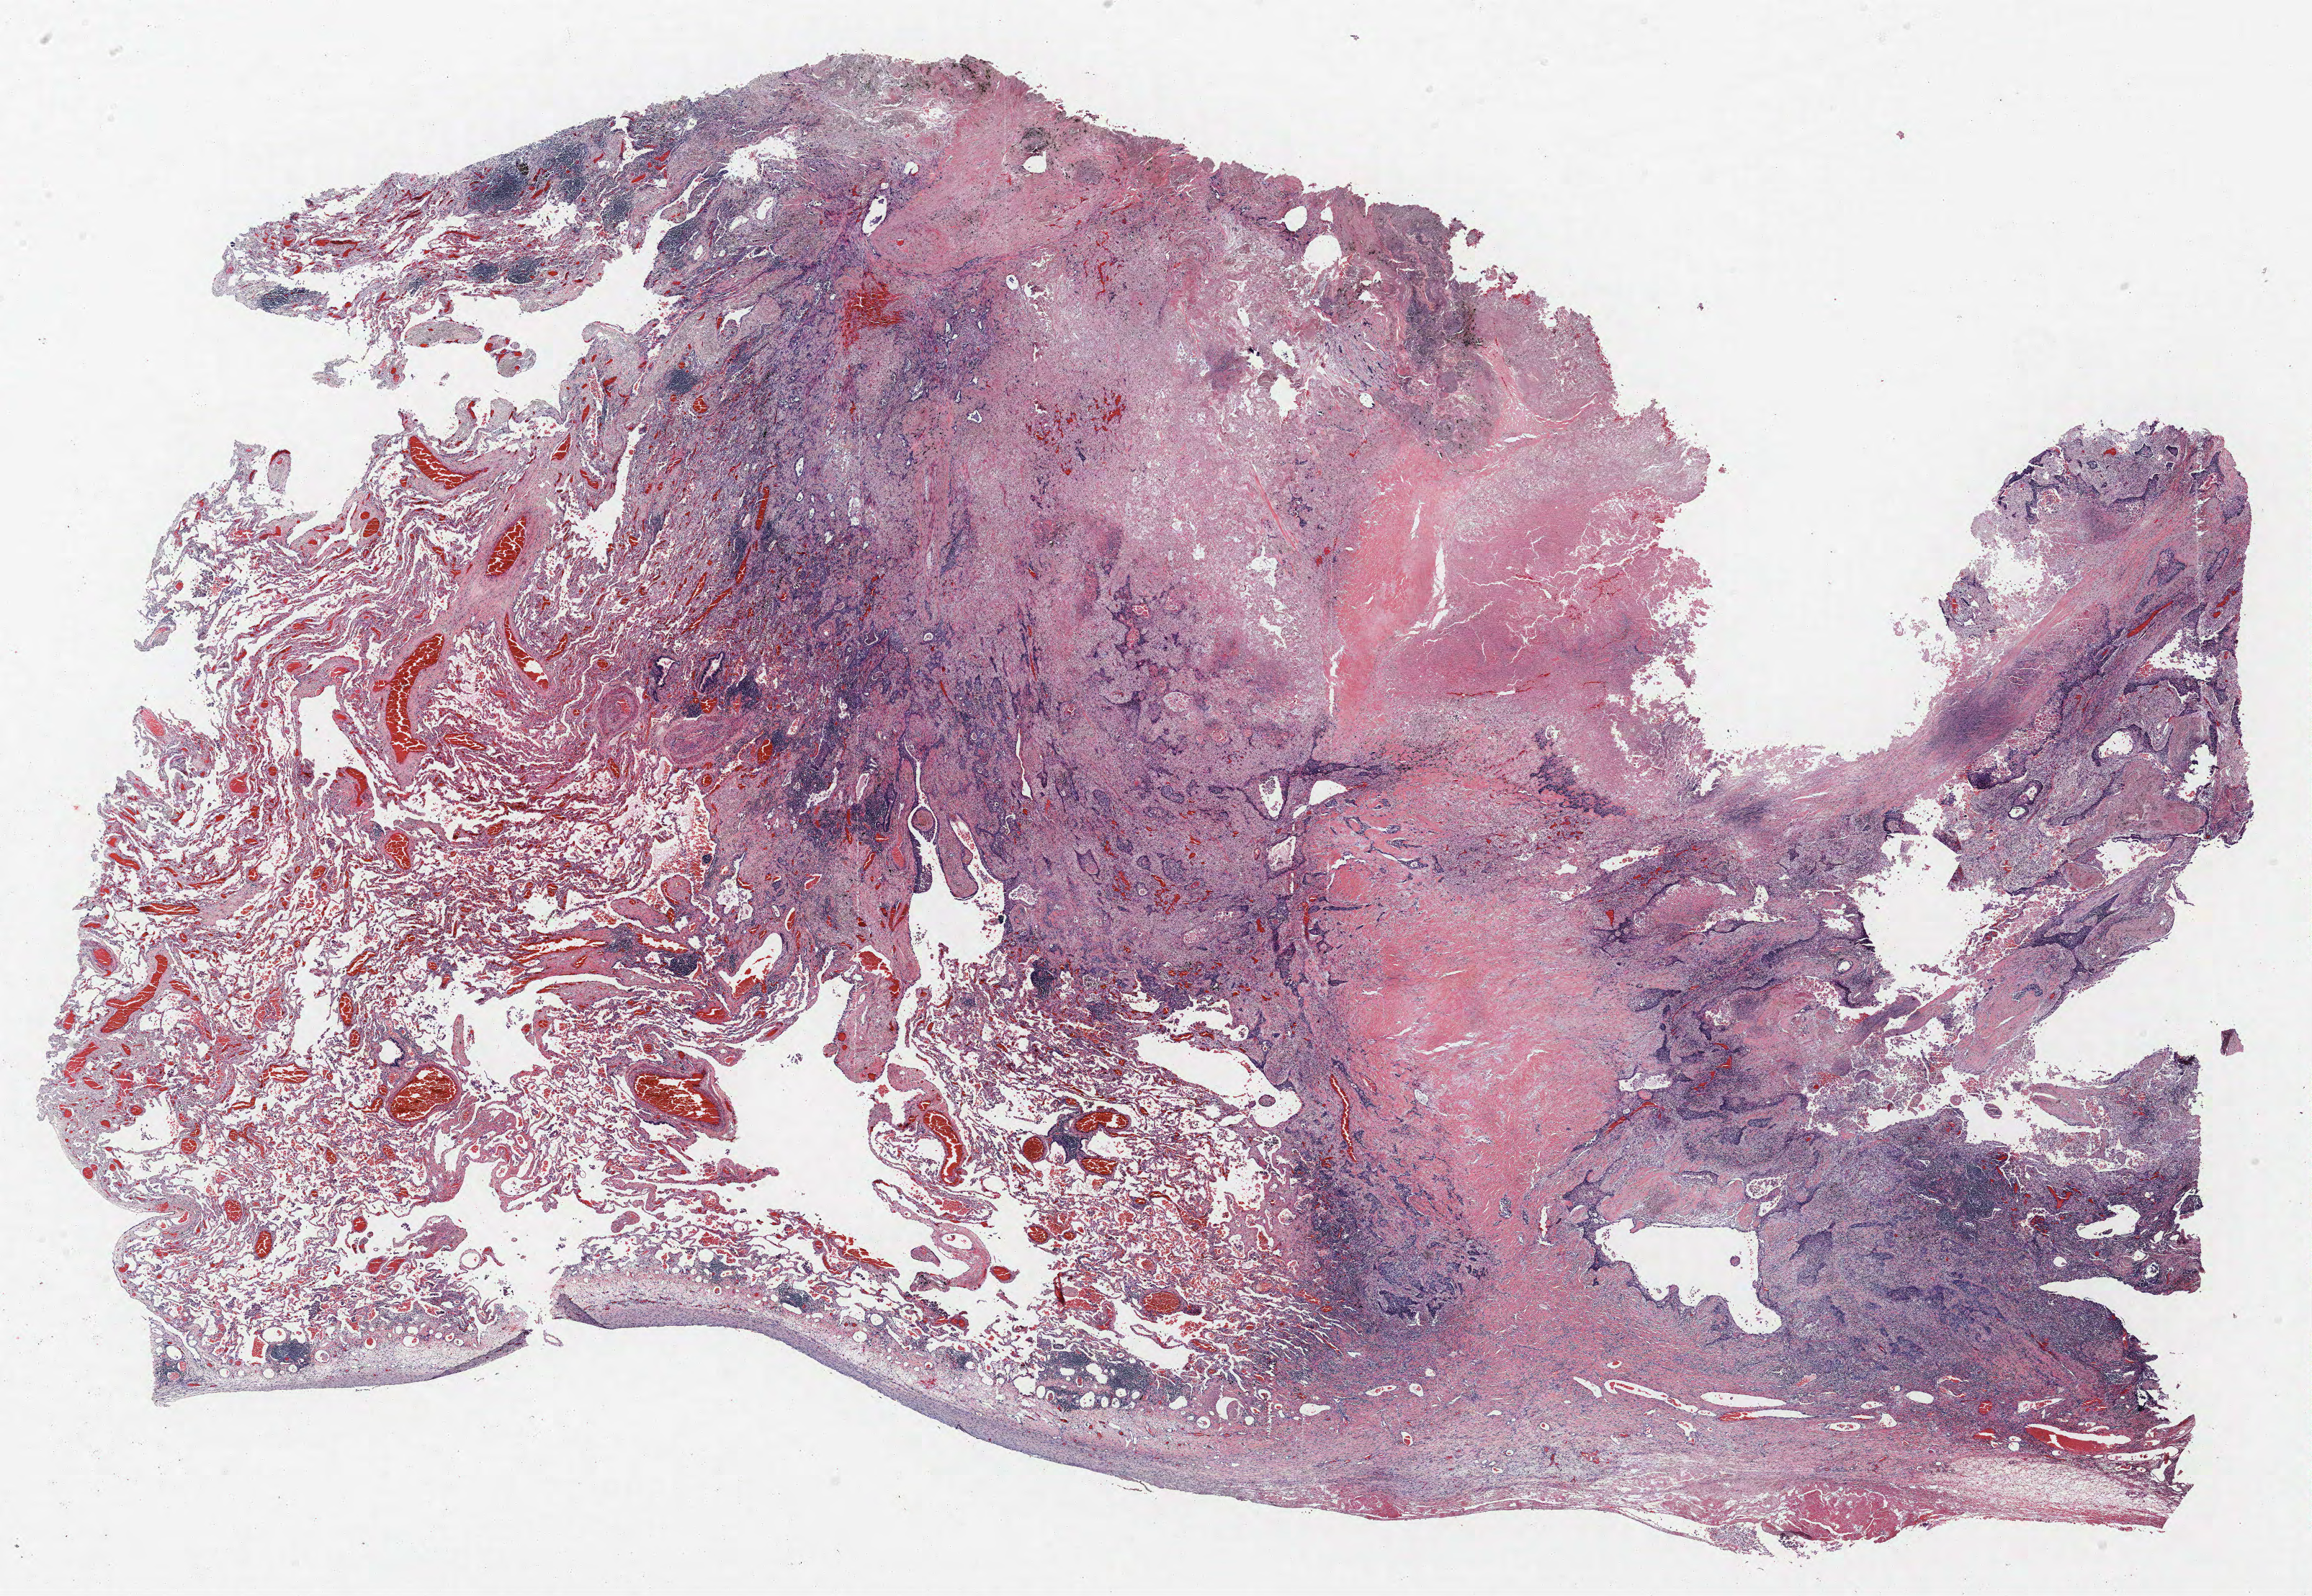
Whole-slide histology image, H&E-stained, low-resolution overview of the scanned area, about 25.7 x 17.7 mm (acquisition: 40x scan); formalin-fixed paraffin-embedded (FFPE) section; lung tissue. Male patient, aged 59 at enrolment. Current smoker at enrolment. Grade: moderately differentiated (G2).
- participant's lung-cancer diagnosis: Squamous cell carcinoma, NOS (ICD-O-3 8070/3)
- ICD-O-3 topography: upper lobe of lung (C34.1)
- stage (AJCC 6th edition): IA
- primary tumour location (clinical record): right upper lobe
- tumour size (pathology): 30 mm